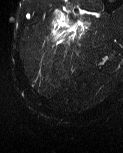
MRI of an extremity soft-tissue mass, one axial slice. Position 8 of 60 along the scan axis. T2-weighted fat-saturated. MR volume resampled by the dataset authors to the PET/CT grid (not the native acquisition matrix). 123 × 153 image matrix, field of view 120 × 149 mm. Male patient. Case-level facts recorded for this patient, not image findings: histological type: pleiomorphic liposarcoma; grade: high; site of the primary tumour: left thigh.
Structures marked on this image (expert contour drawn on MRI and transferred to this co-registered scan by the dataset authors):
- gross tumour volume including surrounding oedema: bounding box <52,11,91,44> (left, top, right, bottom; pixels)